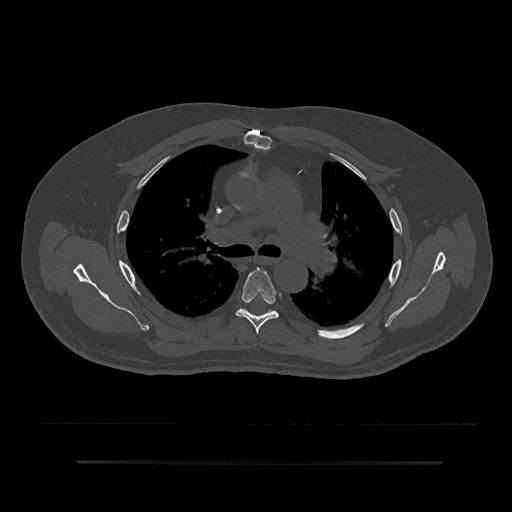
CT including the spine, one axial slice; slice 570 of 797 in the series (ordered by position); reconstruction kernel Br40s/3; 120 kVp; bone window (W 1800 / L 400 HU); 0.5 mm slice thickness; 512 × 512 image matrix, field of view 464 × 464 mm. Patient: male, 59 years. Case-level facts recorded for this patient, not image findings: primary cancer: bile ducts; vertebrae with lytic lesions (as recorded): T10.
Annotated regions visible in this slice (semi-automatically segmented with operator editing):
- T5 vertebra: box from (x=235, y=268) to (x=279, y=334) px
- T6 vertebra: (x=242, y=308)–(x=248, y=312)